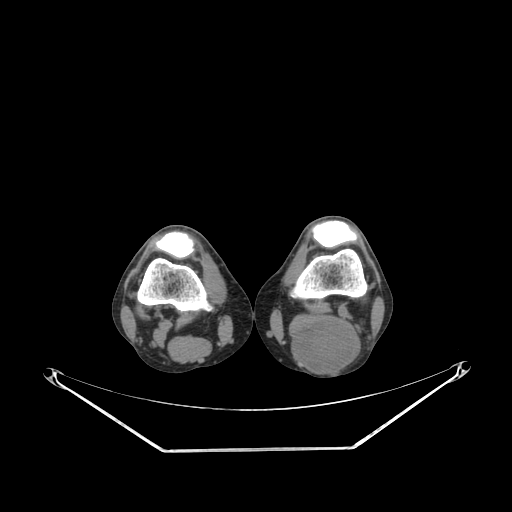
CT of an extremity soft-tissue mass (from a PET/CT study), one axial slice. Slice 185 of 267 in the series (ordered by position). 140 kVp. Soft-tissue window (W 400 / L 40 HU). 3.75 mm slice thickness. 512 × 512 image matrix. Male patient. Case-level facts recorded for this patient, not image findings: histological type: synovial sarcoma; site of the primary tumour: left poplietal fossa.
Outlined on this slice (expert contour drawn on MRI and transferred to this co-registered scan by the dataset authors):
- gross tumour volume (mass): box from (x=290, y=319) to (x=362, y=373) px